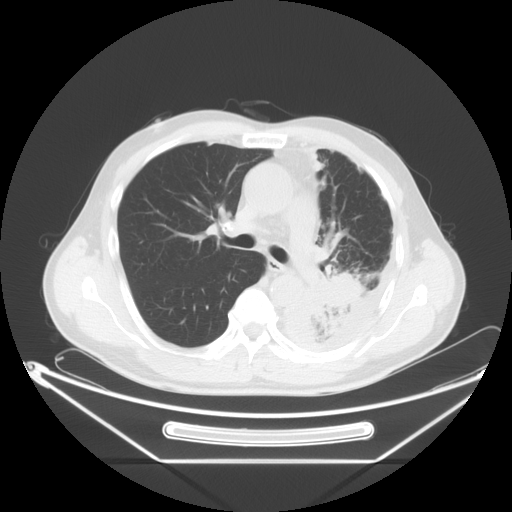
Chest CT, one axial slice. Reconstruction kernel STANDARD. Lung window (W 1500 / L -600 HU). 5 mm slice thickness. 512 × 512 image matrix. Patient: male, 60 years. From the clinical record (not read from this slice): clinical TNM (as recorded): T4 N1 M1.
Structures marked on this image (bounding box drawn by a radiologist):
- lung tumour (recorded histology: adenocarcinoma): box from (x=298, y=250) to (x=371, y=336) px